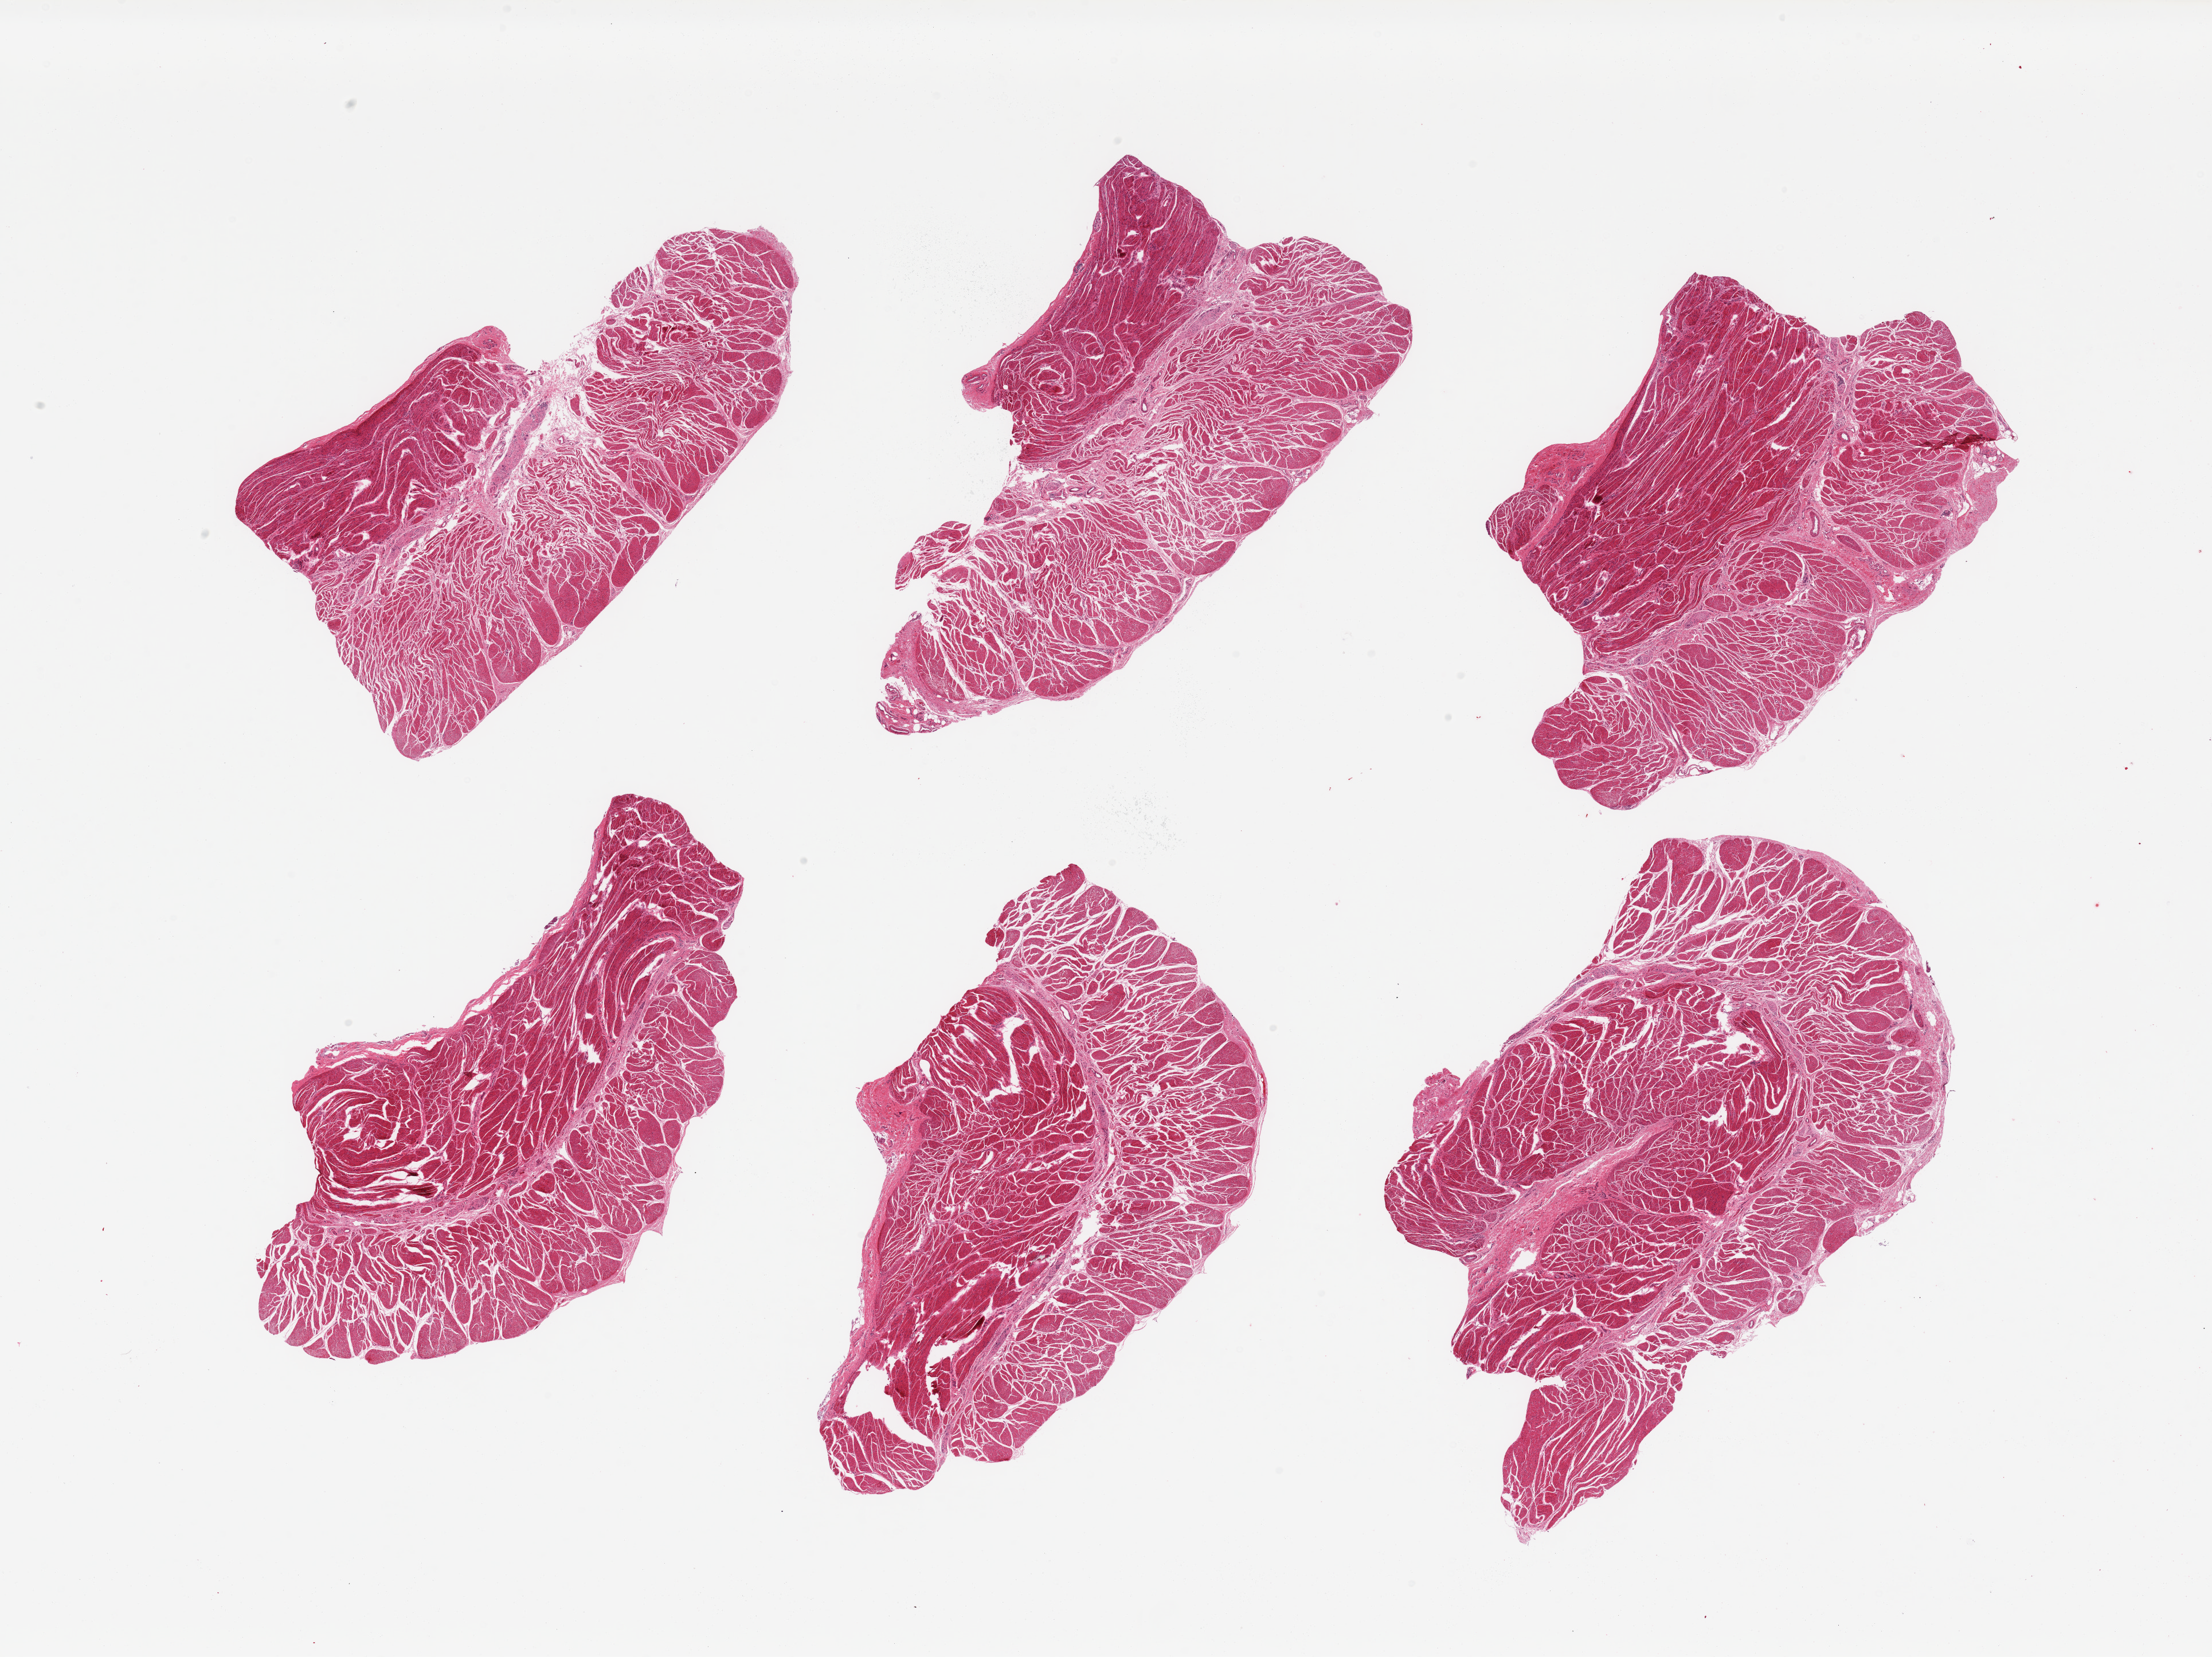
Whole-slide image, haematoxylin and eosin stain, low-resolution overview of the scanned area, about 30.5 x 22.9 mm (acquisition: 20x scan); PAXgene-fixed, paraffin-embedded tissue; section of gastroesophageal junction (target tissue); tissue donor sample.
Pathologist's review note for this sample: 6 pieces; well trimmed target muscularis.